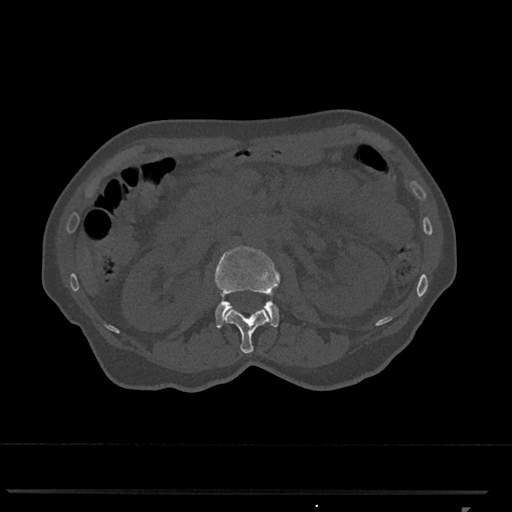
CT including the spine, one axial slice; reconstruction kernel Br40s/3; 120 kVp; bone window (W 1800 / L 400 HU); 0.5 mm slice thickness; 512 × 512 image matrix, field of view 380 × 380 mm. Patient: female, 62 years. Case-level facts recorded for this patient, not image findings: primary cancer: renal.
Outlined on this slice (semi-automatically segmented with operator editing):
- L1 vertebra: box from (x=222, y=306) to (x=272, y=354) px
- L2 vertebra: (x=214, y=246)–(x=280, y=328)